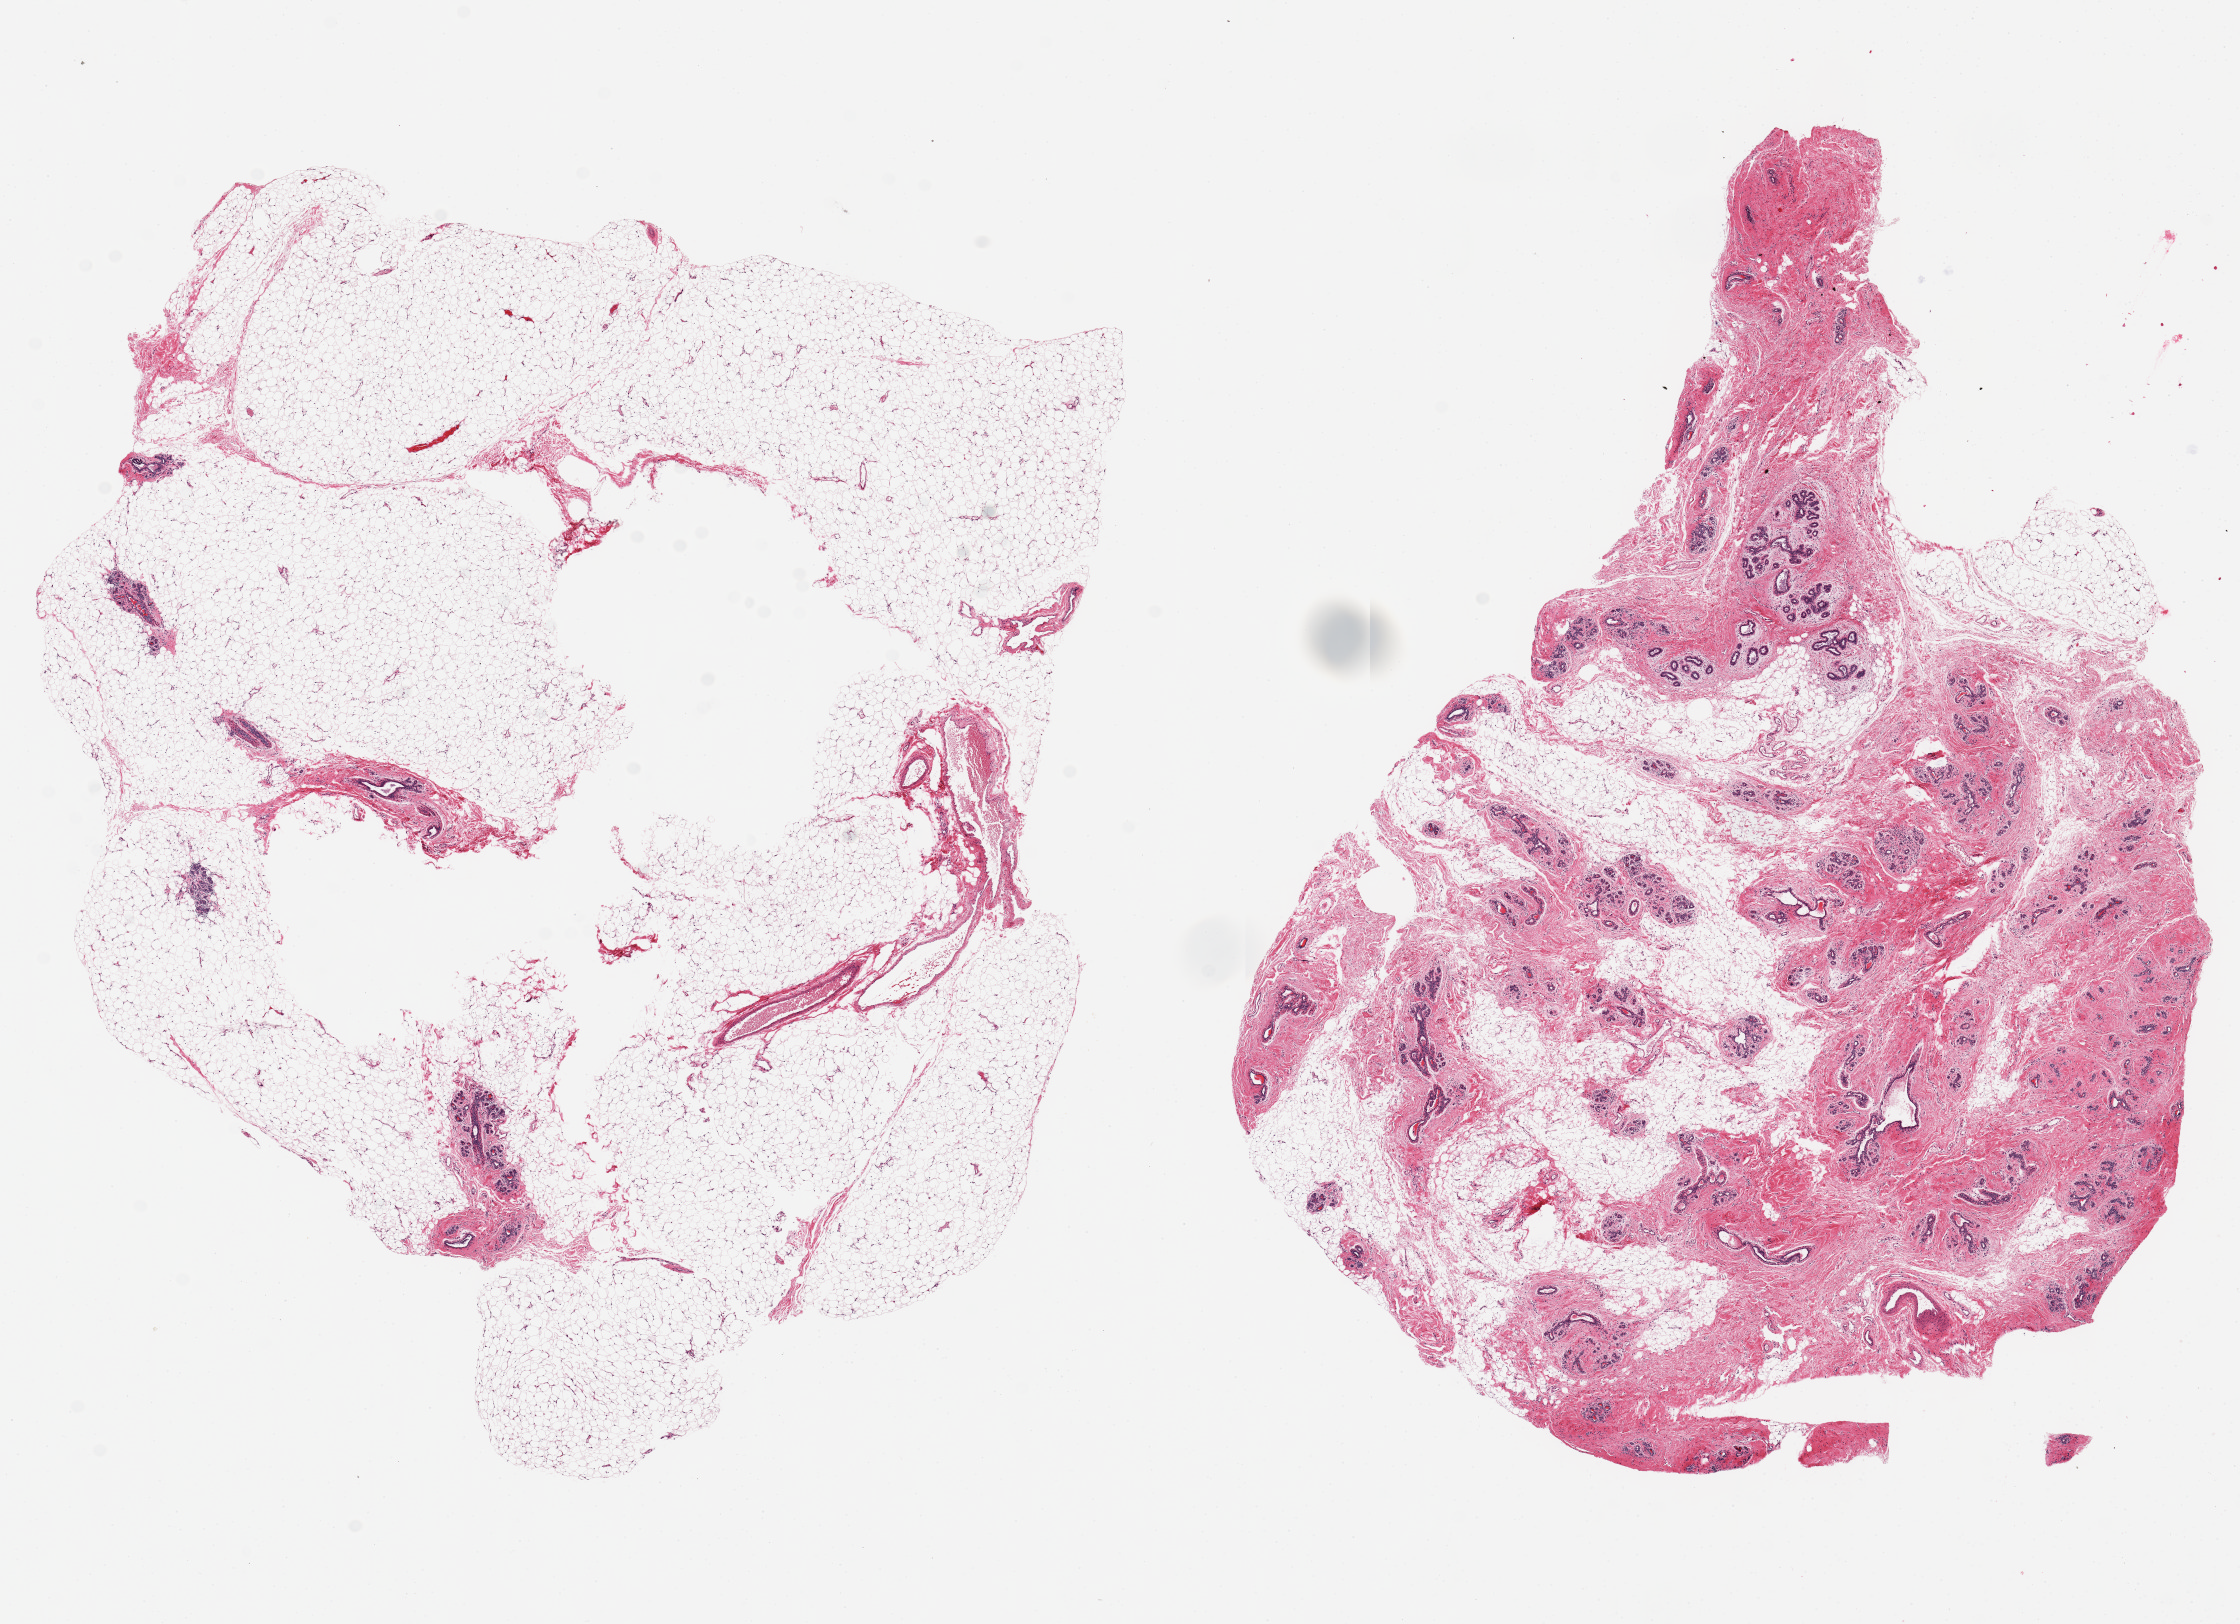
H&E whole-slide image — a low-resolution overview of the entire scanned area, about 17.7 x 12.8 mm; PAXgene-fixed paraffin-embedded (PFPE) section; target tissue: breast; tissue donor sample.
- review note (as recorded): 2 ~10x8mm pieces, both with atrophic TDLUs, one with more adipose tissue; the other with more stroma